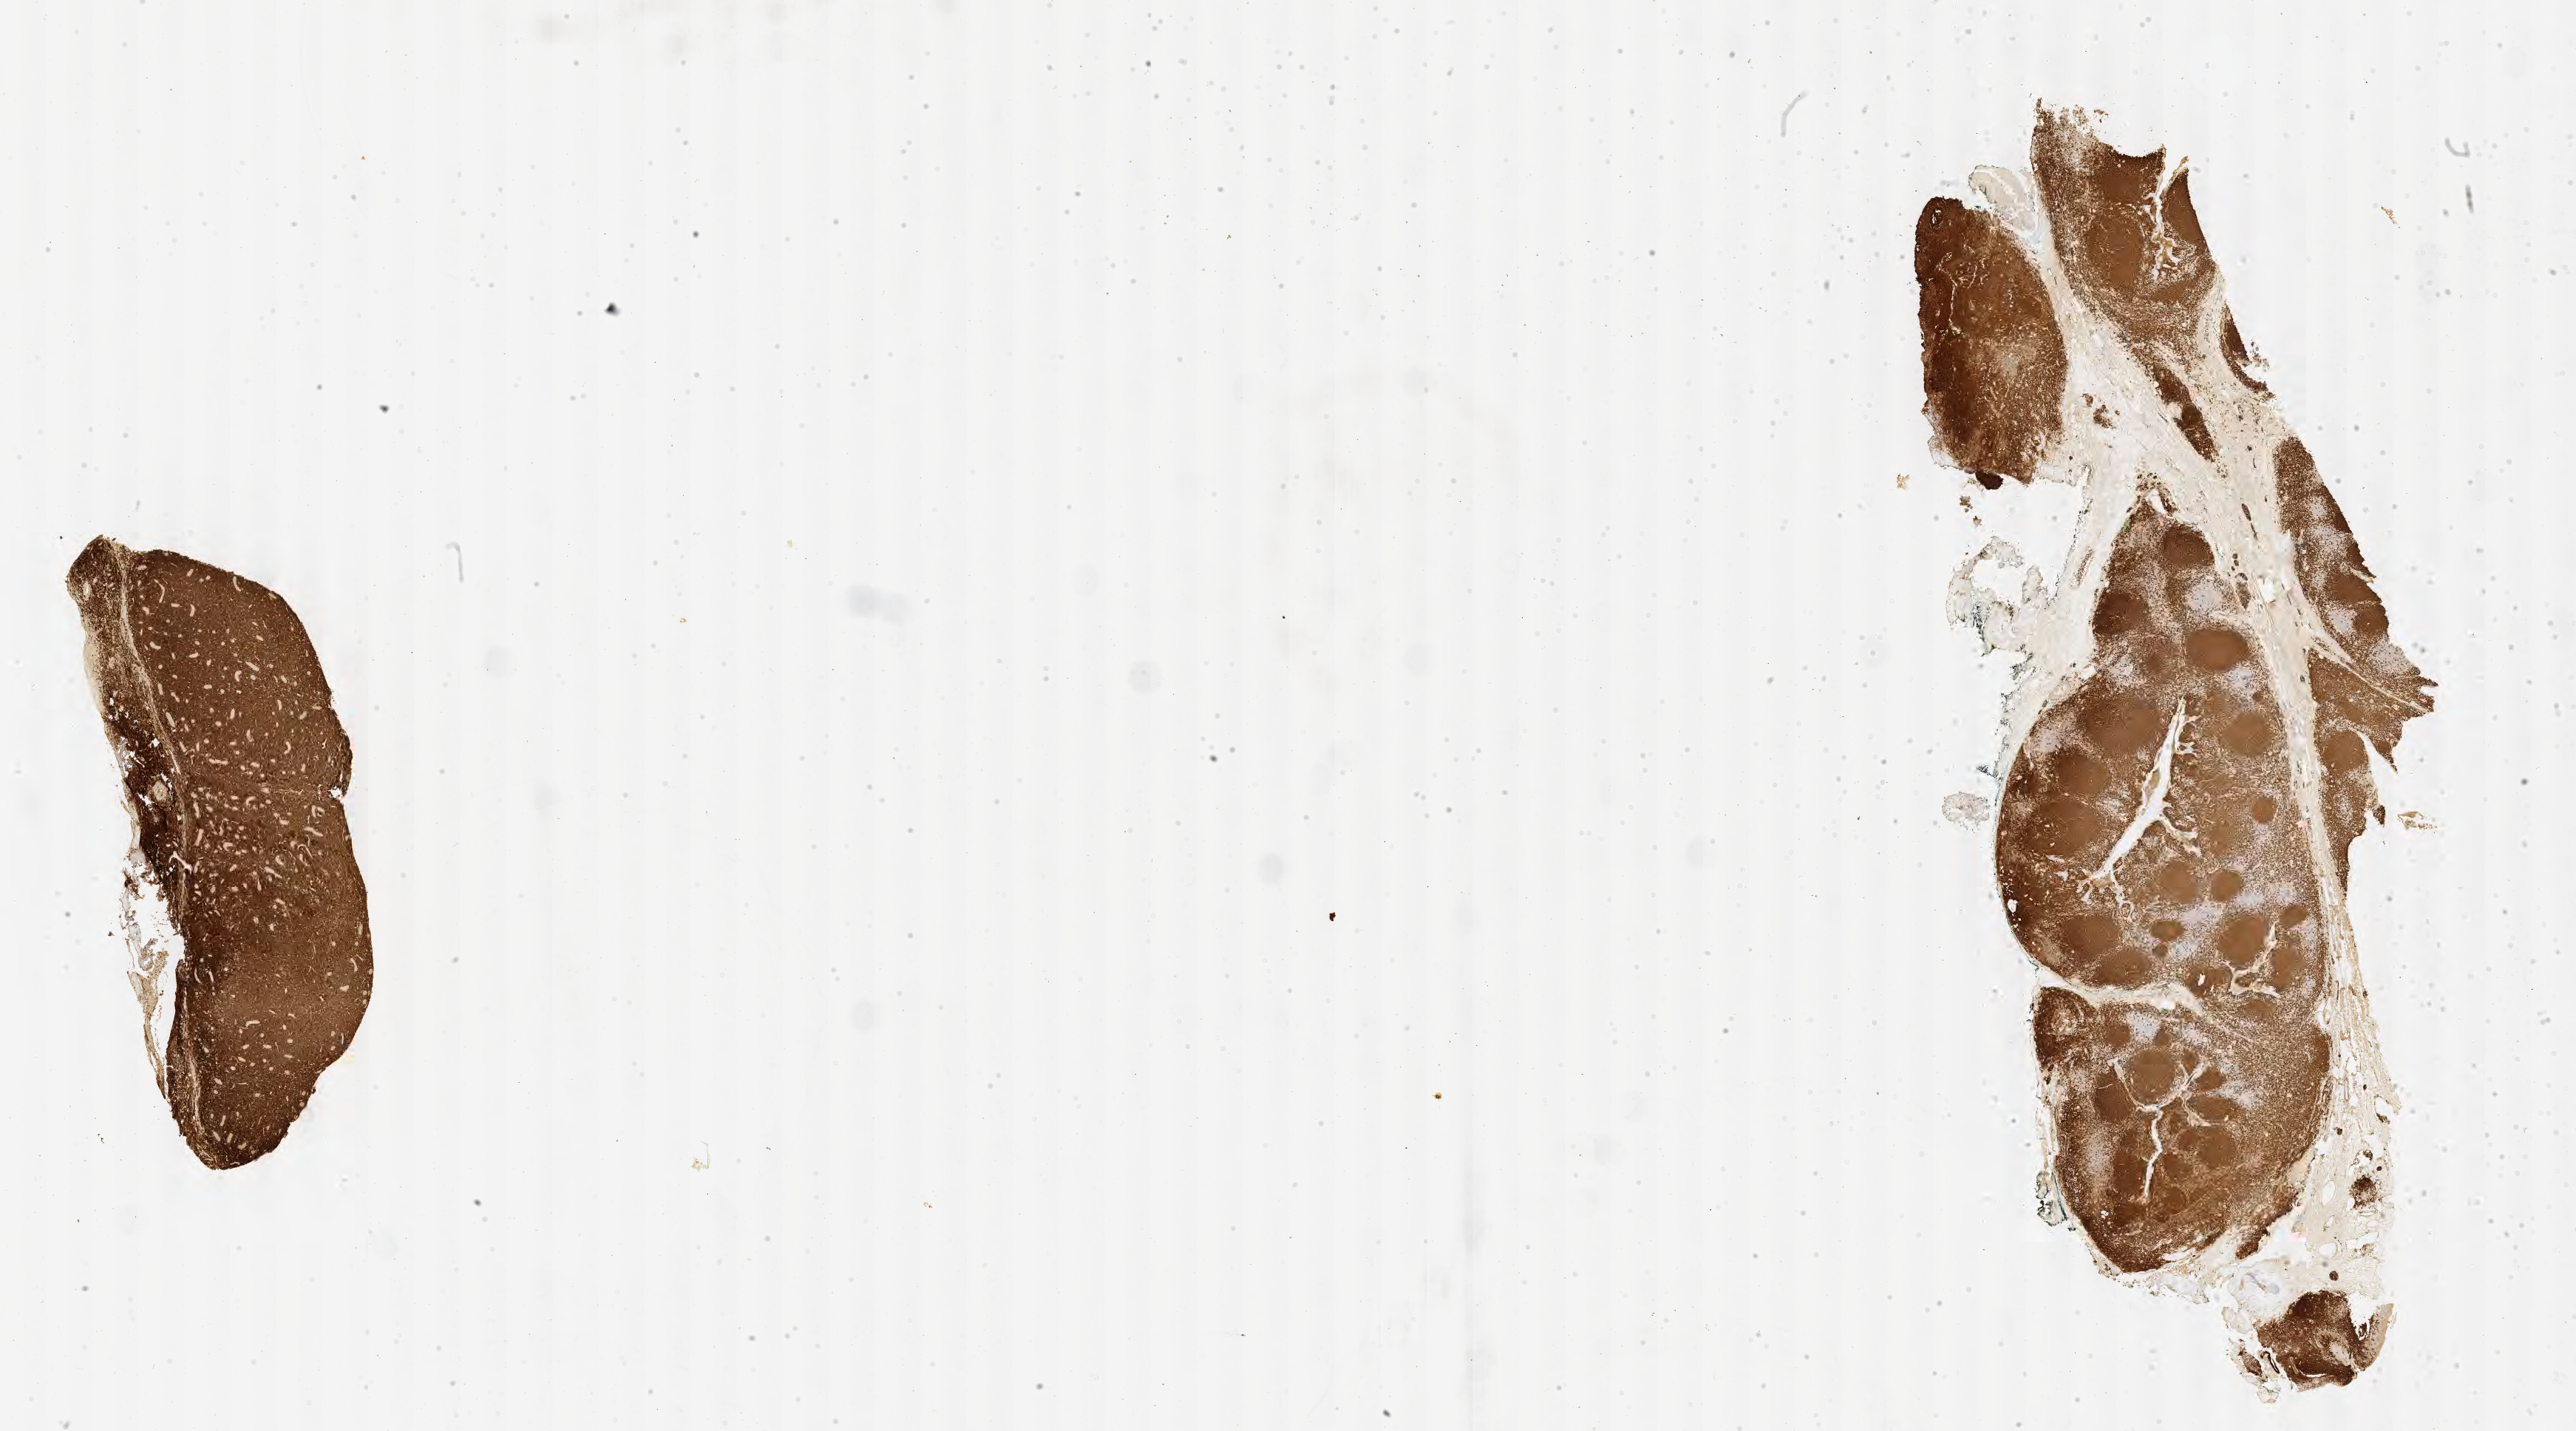
Immunohistochemistry (IHC) whole-slide image stained for CD20 — low-resolution overview of the scanned area, about 28.2 x 15.7 mm. Specimen: tumor tissue. Anatomic site: testis. Male, age 8 years at initial diagnosis.
Histologic diagnosis: Burkitt lymphoma, NOS.